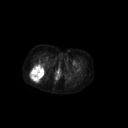
FDG PET of an extremity soft-tissue mass (from a PET/CT study), one axial slice; 128 × 128 image matrix. Female patient, age 70 years. Case-level facts recorded for this patient, not image findings: histological type: synovial sarcoma; grade: intermediate; site of the primary tumour: right buttock.
Annotated regions visible in this slice (expert contour drawn on MRI and transferred to this co-registered scan by the dataset authors):
- gross tumour volume including surrounding oedema: box from (x=30, y=64) to (x=45, y=81) px
- gross tumour volume (mass): (x=30, y=64)–(x=45, y=81)